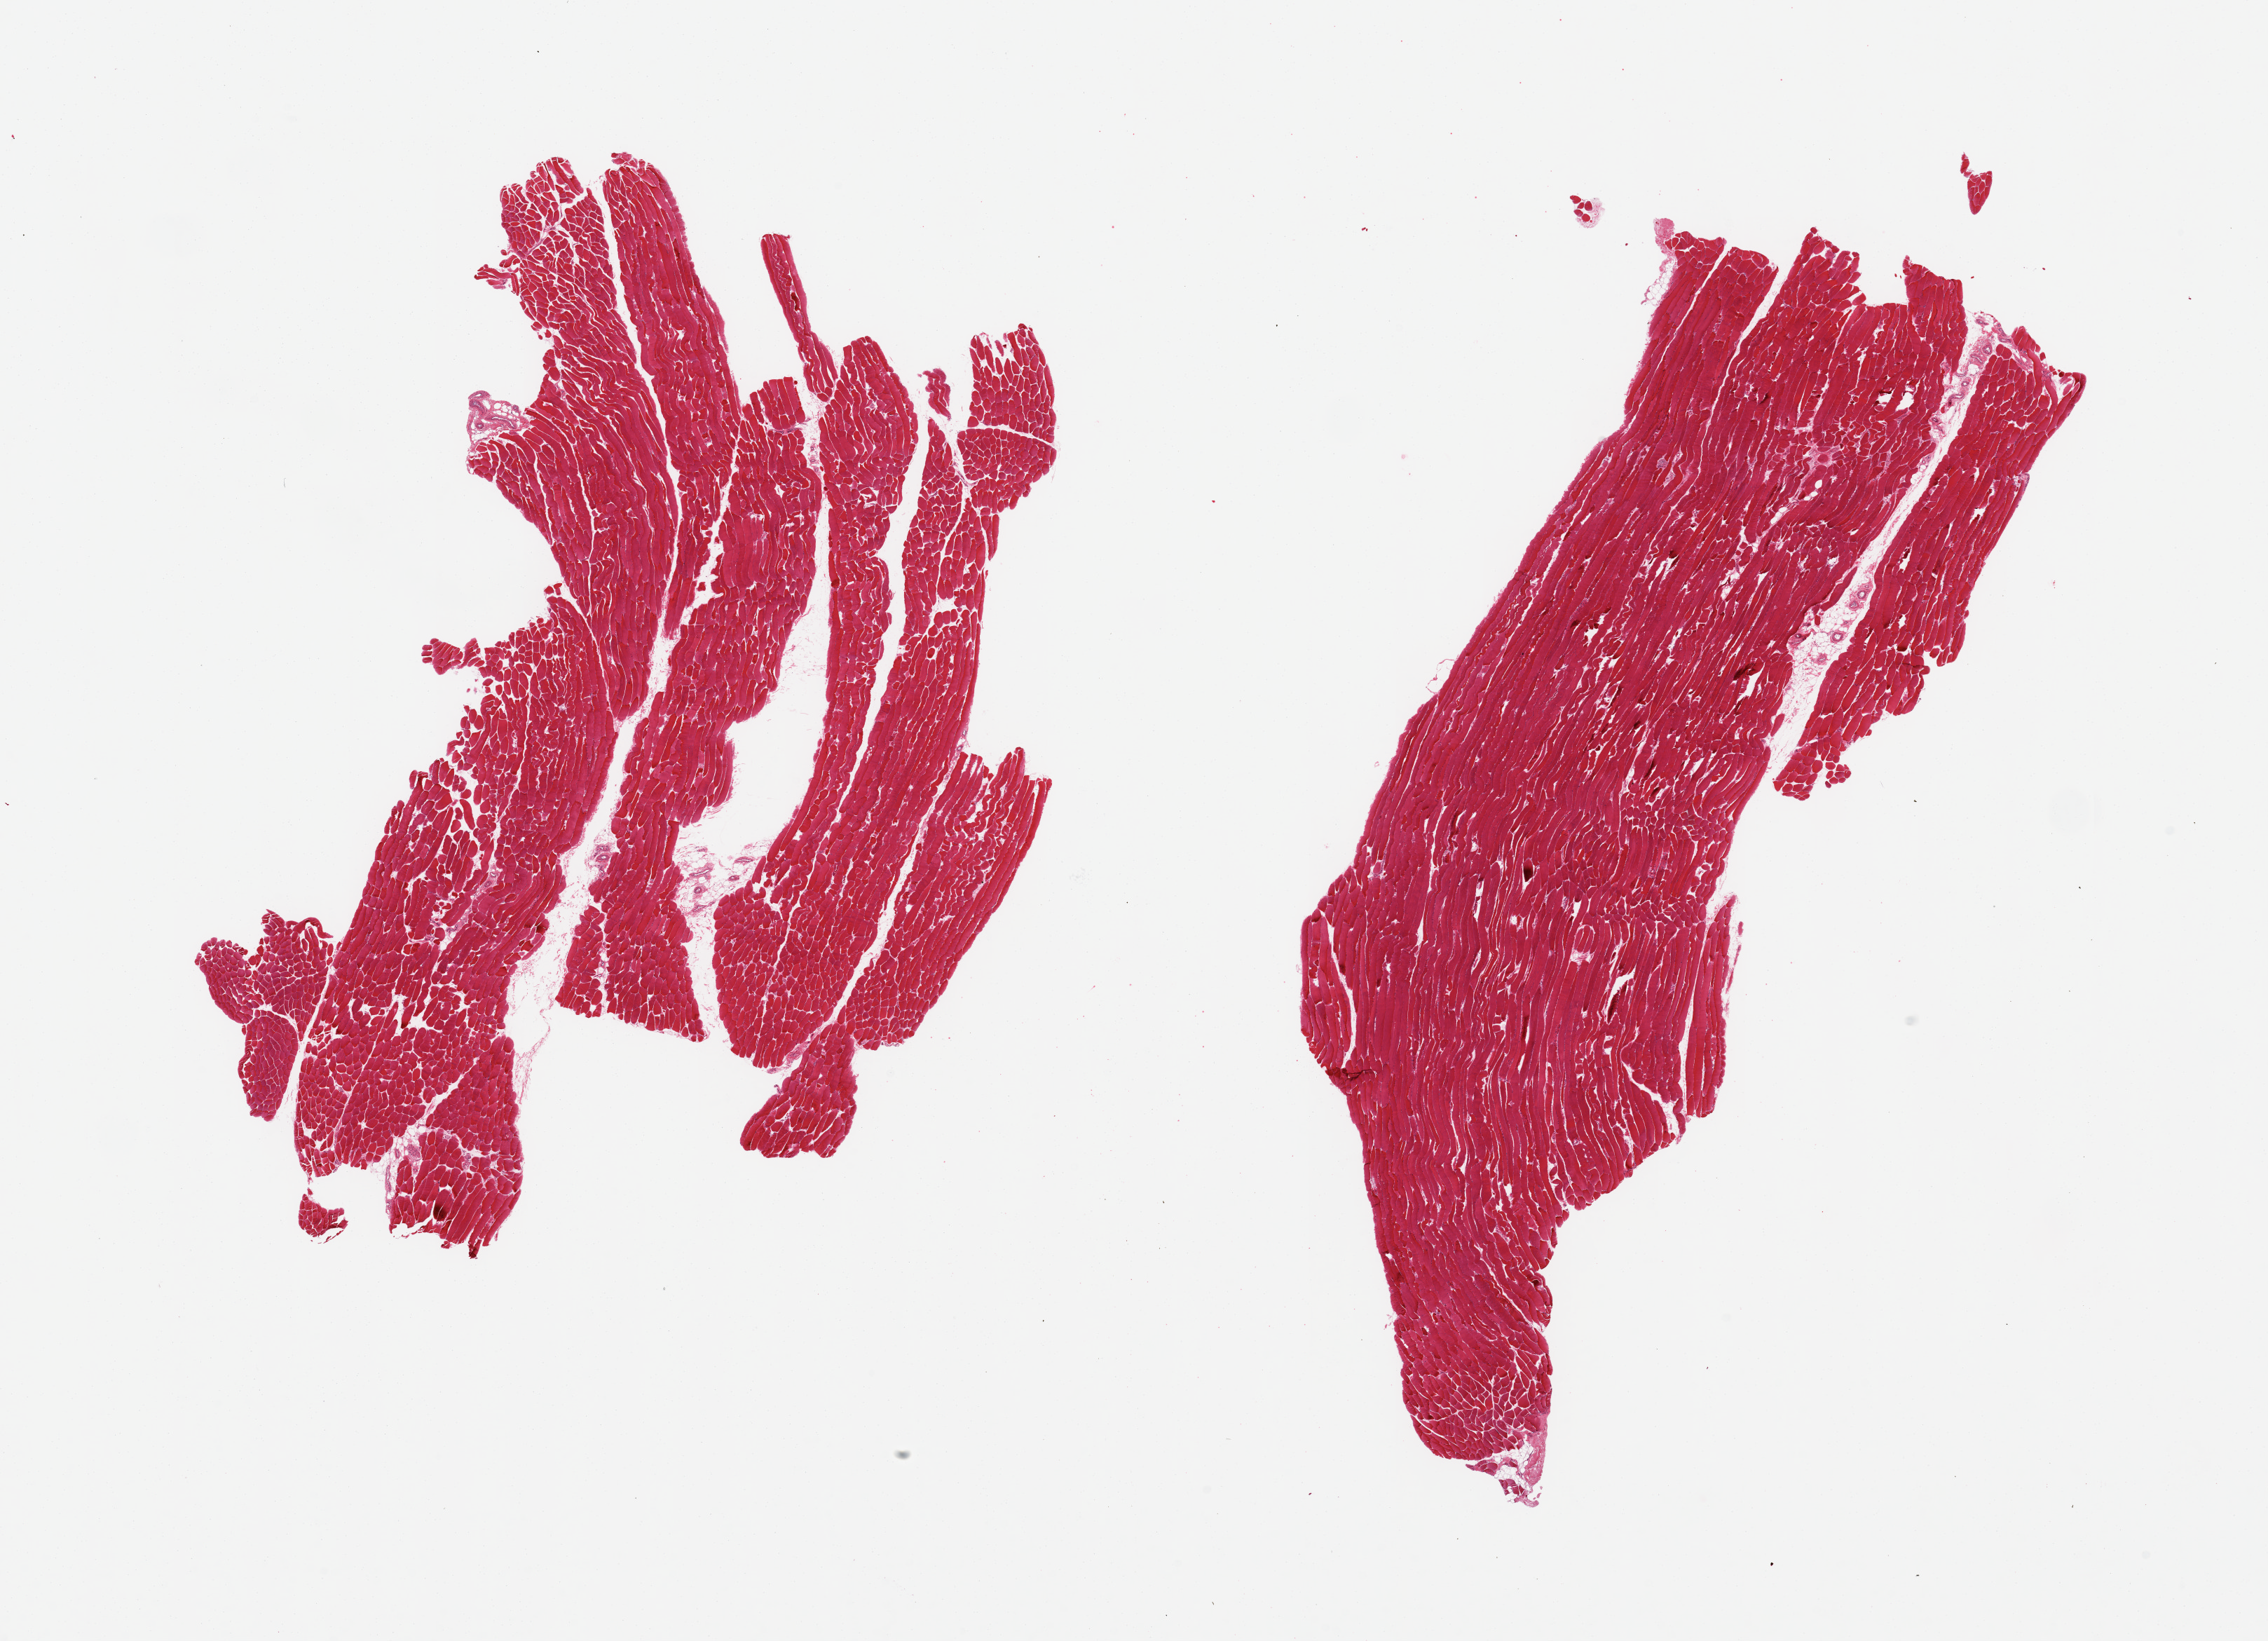
Digitized H&E-stained section, brightfield, shown as a low-resolution overview of the whole scanned area (about 25.6 x 18.5 mm, from a 20x scan). PAXgene-fixed paraffin-embedded (PFPE) section. Sampled site (target tissue): skeletal muscle. Tissue donor sample. Donor sex: male.
Reviewer comment on this tissue sample: 2 pieces; <1% fat content.